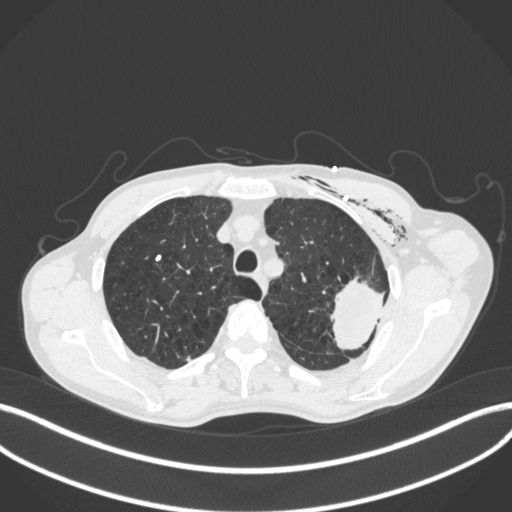
Chest CT, one axial slice. Slice 325 of 416 in the series (ordered by position). Reconstruction kernel B31f. Lung window (W 1500 / L -600 HU). 1 mm slice thickness. 512 × 512 image matrix, field of view 400 × 400 mm. Patient: male, 58 years. From the clinical record (not read from this slice): clinical TNM (as recorded): T3 N0 M0.
Annotated regions visible in this slice (rectangle marked by the reading radiologist):
- lung tumour (recorded histology: adenocarcinoma): bounding box <330,273,390,358> (left, top, right, bottom; pixels)